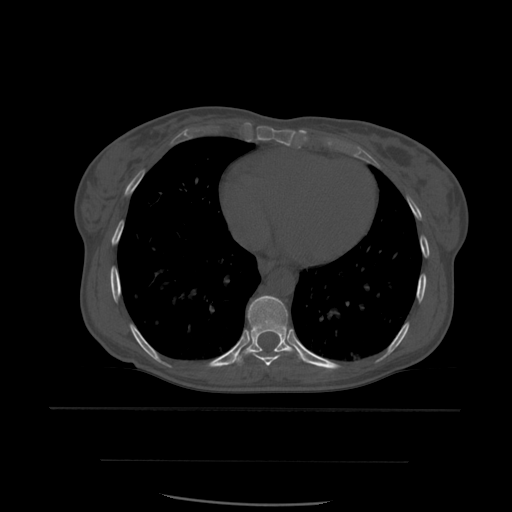
CT including the spine, one axial slice. Bone window (W 1800 / L 400 HU). 512 × 512 image matrix. Patient age 48 years. Case-level facts recorded for this patient, not image findings: primary cancer: lung; vertebrae with lytic lesions (as recorded): T11.
Structures marked on this image (semi-automatic segmentation, software-assisted and operator-edited):
- T8 vertebra: bounding box (x1, y1, x2, y2) in pixels: (248, 351, 281, 368)
- T9 vertebra: (234, 296, 311, 366)